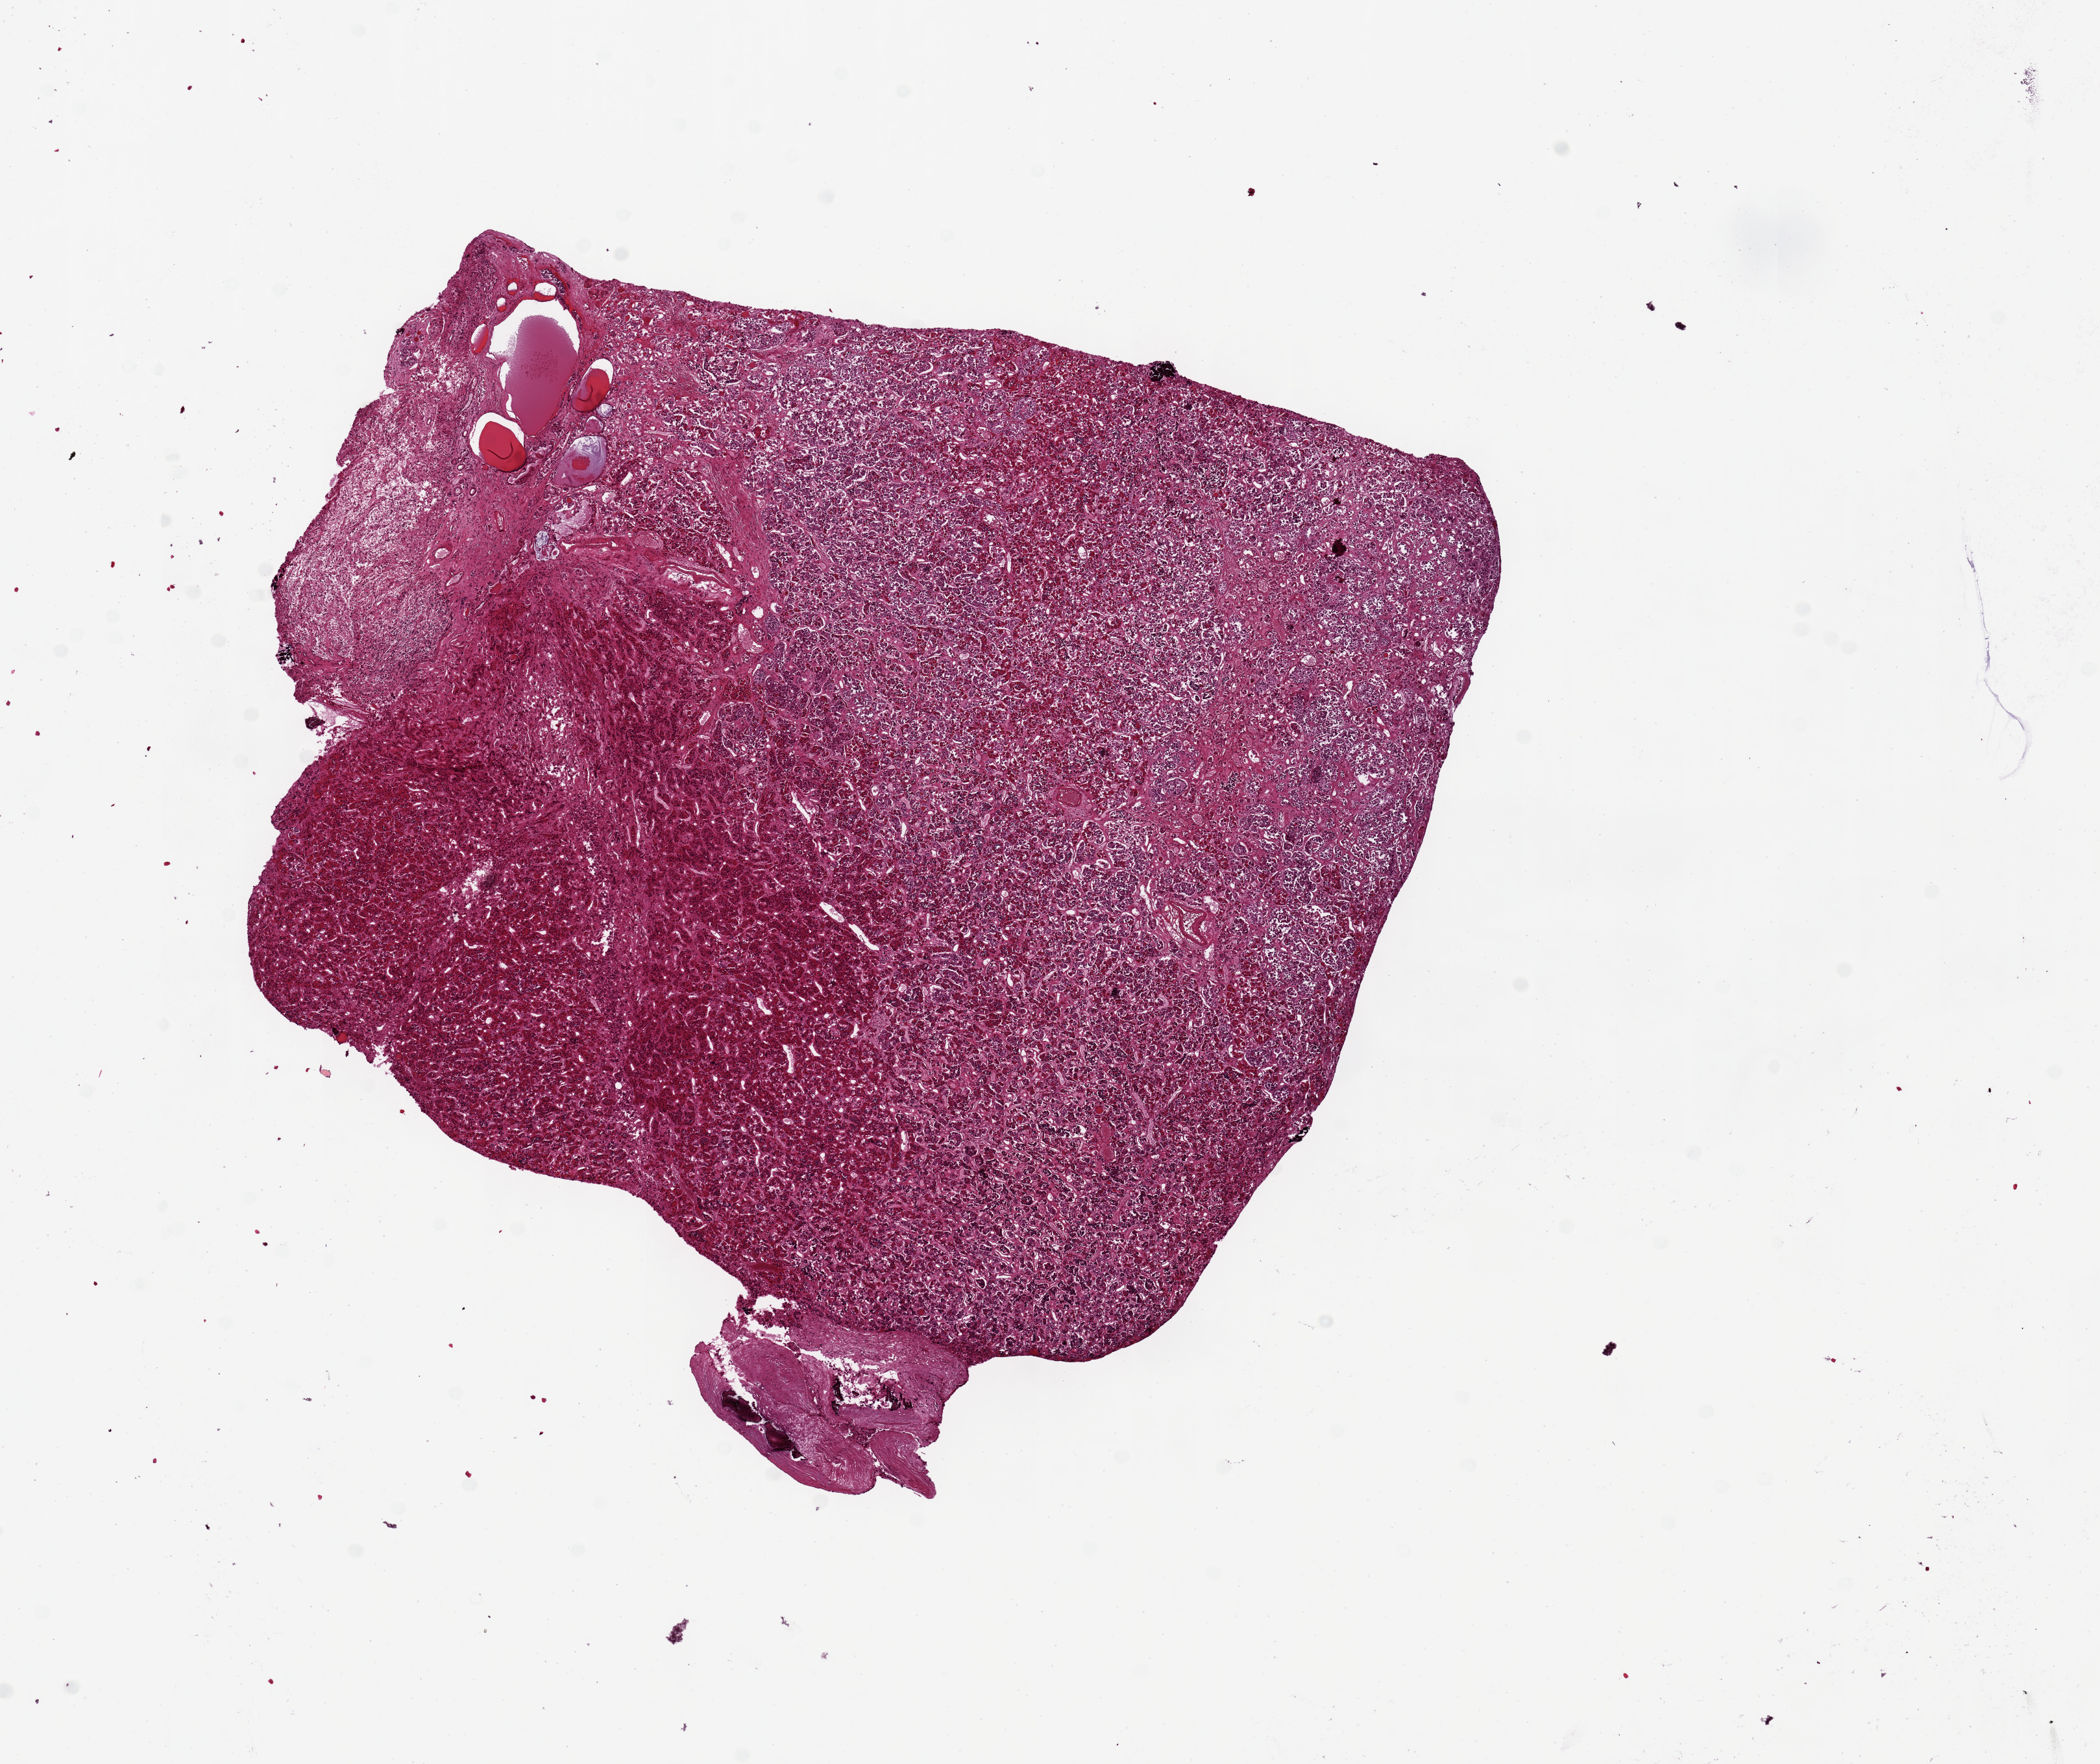
H&E whole-slide image — shown as a low-resolution overview of the whole scanned area (about 12.8 x 10.7 mm). PAXgene-fixed, paraffin-embedded tissue. Target tissue: pituitary. Donor tissue sample. Donor sex: female.
- review note (as recorded): 1 piece 7x6 mm; 3x1 mm is posterior